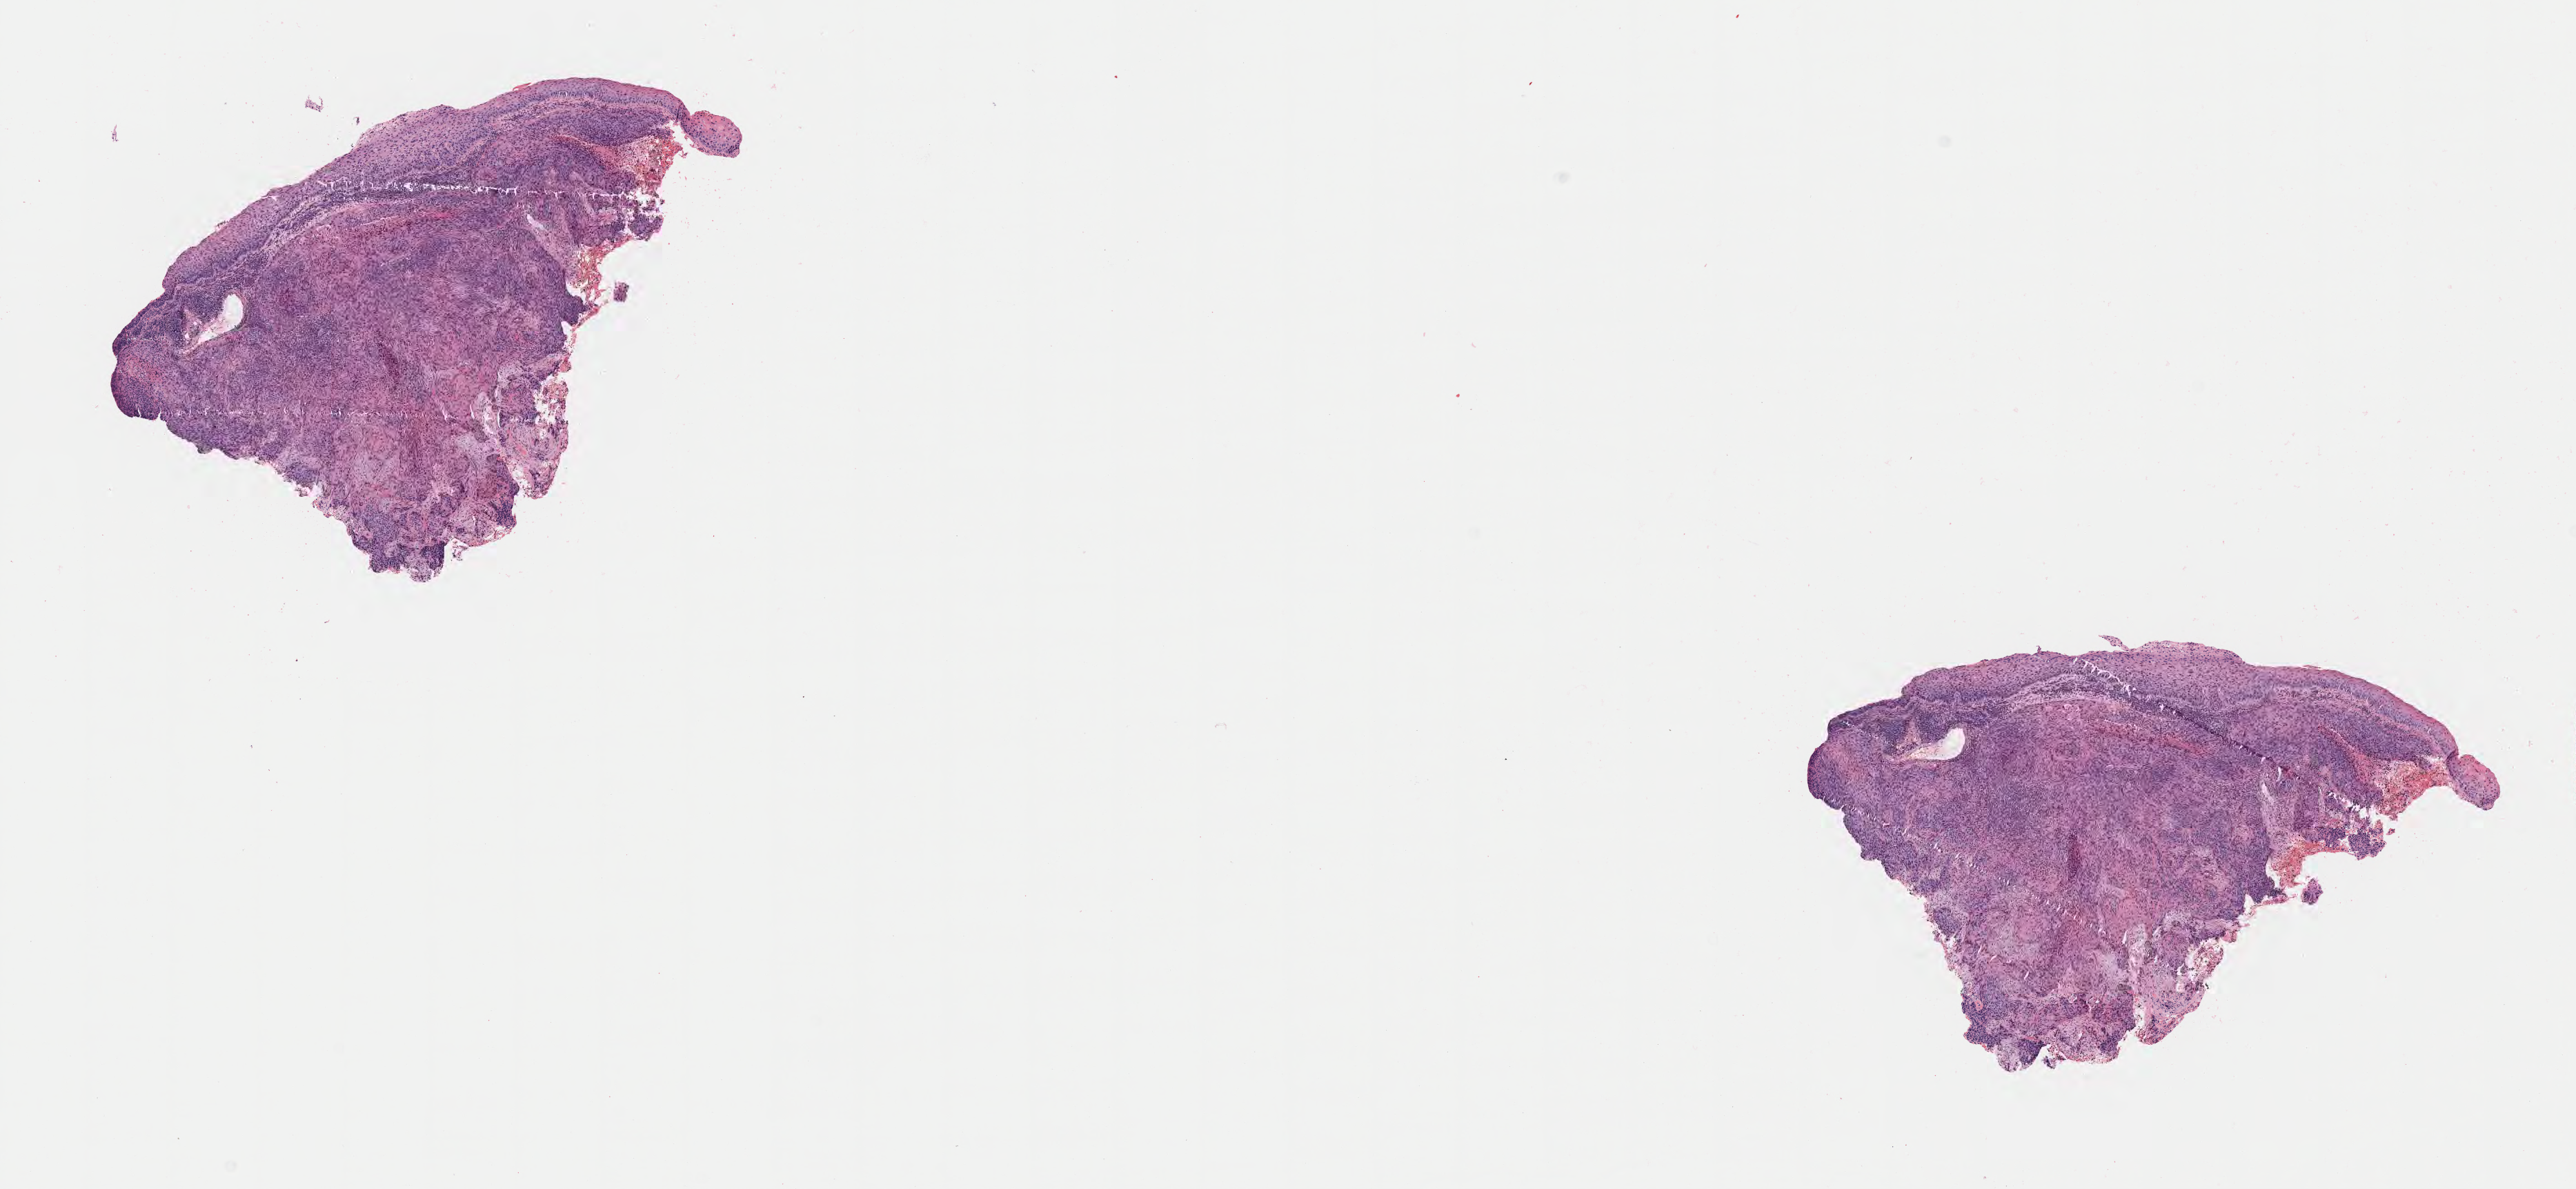
Whole-slide image, hematoxylin and eosin (H&E) stain — low-resolution overview of the scanned area, about 15.1 x 7.0 mm; tumor tissue; anatomic site: cervix. Patient female; age 36 years.
Histologic diagnosis: Squamous cell carcinoma, large cell, nonkeratinizing, NOS.